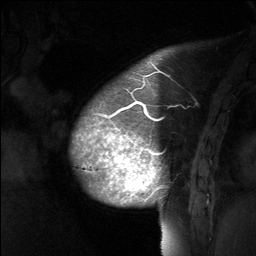
Breast MRI (dynamic contrast-enhanced), one sagittal slice. Slice 14 of 64 in the series (ordered by position). Dynamic contrast-enhanced study with each time point stored as its own series, time point 2 of 3 at this slice position (early post-contrast, ordered by acquisition time). 1.5 T. TE 4.8 ms, TR 27 ms. 2 mm slice thickness. 256 × 256 image matrix, field of view 200 × 200 mm. Female patient, age 39 years. Case-level facts recorded for this patient, not image findings: setting: breast cancer imaged before/during neoadjuvant chemotherapy; receptor status: HER2-positive.
Annotated regions visible in this slice (semi-automatic segmentation, software-assisted and operator-edited):
- analysis volume of interest (the breast-tissue region the enhancement analysis was run in; not a lesion): bounding box <70,69,202,224> (left, top, right, bottom; pixels)
- tumour enhancement mask (voxels above the 90 % enhancement threshold inside the analysis volume of interest): <82,101,163,198>